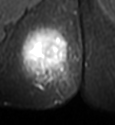
MRI of an extremity soft-tissue mass, one axial slice. STIR. MR volume resampled by the dataset authors to the PET/CT grid (not the native acquisition matrix). 3.27 mm slice thickness. 115 × 125 image matrix, field of view 112 × 122 mm. Female patient. Case-level facts recorded for this patient, not image findings: histological type: epithelioid sarcoma; grade: intermediate; site of the primary tumour: right buttock.
Structures marked on this image (expert contour drawn on MRI and transferred to this co-registered scan by the dataset authors):
- gross tumour volume including surrounding oedema: bounding box [x1, y1, x2, y2] px = [17, 25, 77, 97]
- gross tumour volume (mass): [22, 30, 68, 74]